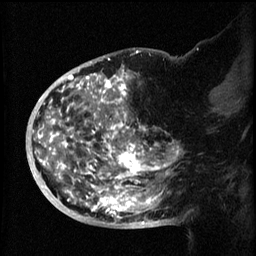
Breast MRI (dynamic contrast-enhanced), one sagittal slice. 3 images stored at this slice position (order not interpretable as contrast timing). 1.5 T. TE 4.2 ms, TR 8.2 ms. 2 mm slice thickness. 256 × 256 image matrix. Female patient, age 50 years.
Structures marked on this image (semi-automatic segmentation, software-assisted and operator-edited):
- analysis volume of interest (the breast-tissue region the enhancement analysis was run in; not a lesion): box from (x=44, y=72) to (x=173, y=219) px
- tumour enhancement mask (voxels above the 70 % enhancement threshold inside the analysis volume of interest): (x=44, y=72)–(x=171, y=219)